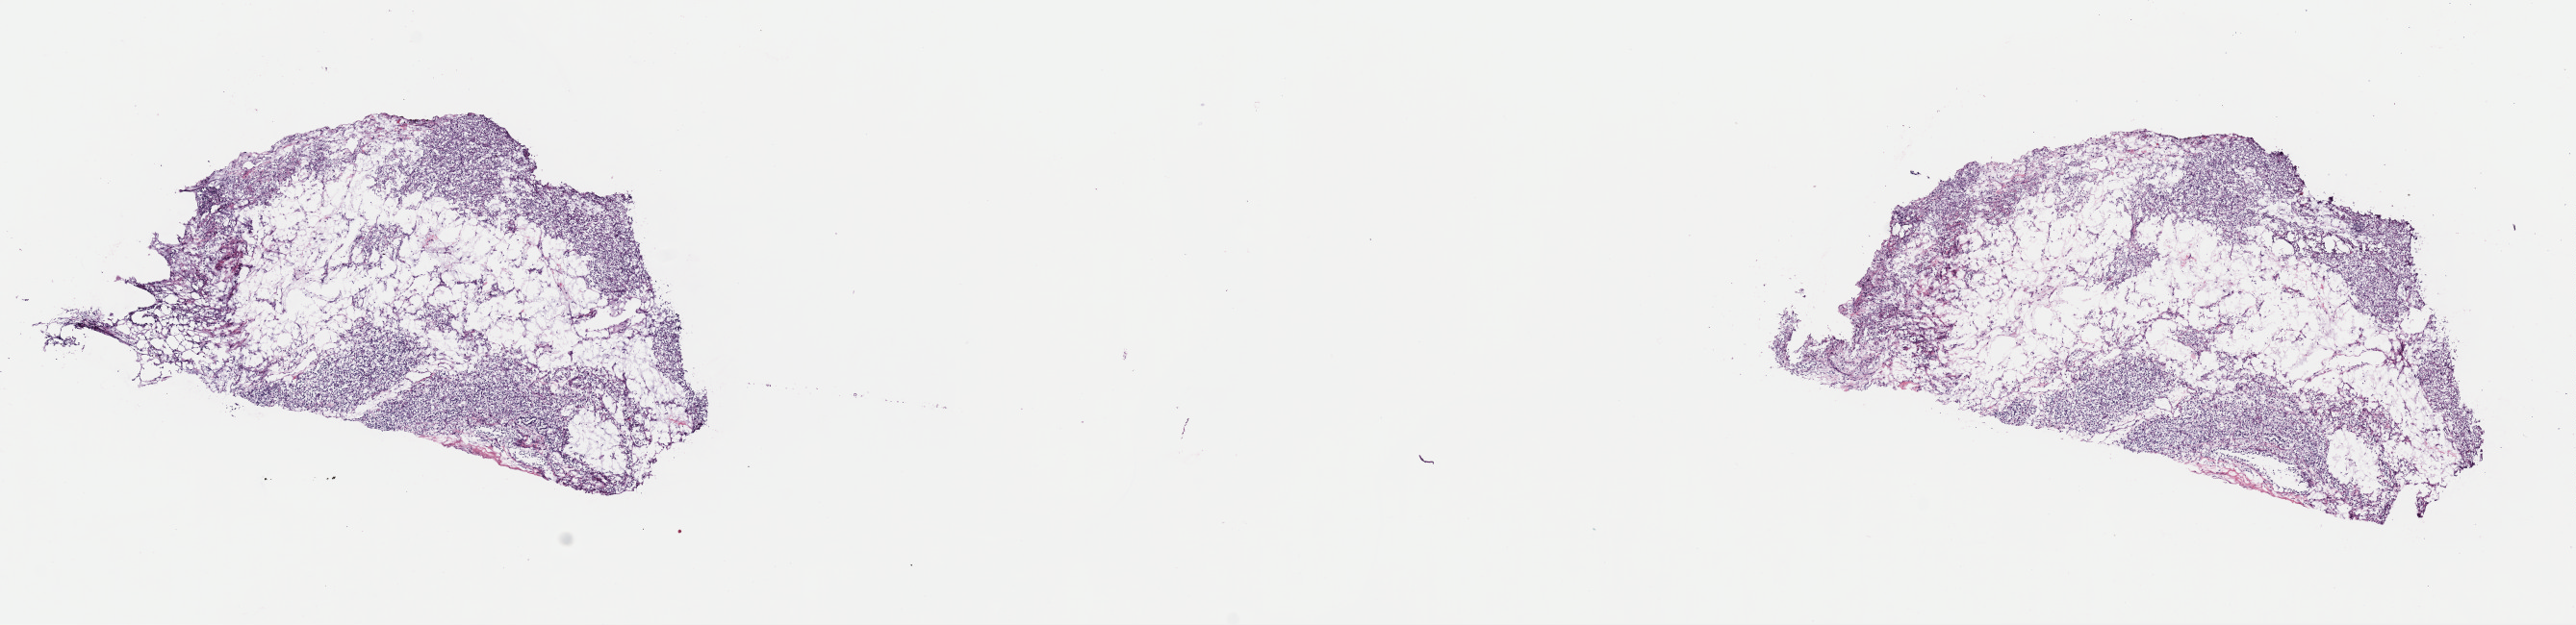
Hematoxylin and eosin (H&E) stained whole-slide image, a low-resolution overview of the entire scanned area, about 21.1 x 5.1 mm (slide scanned at 40x); frozen section from the top of the tissue portion; sample: primary tumour, kidney. Male, age 78 years at initial diagnosis. Histologic grade: G2 (moderately differentiated). Pathologist review of this section (percent, as recorded): tumour cells 85%, tumour nuclei 85%, normal cells 0%, stromal cells 15%, necrosis 0%. Inflammatory infiltration, as recorded: lymphocyte infiltration 0%, monocyte infiltration 0%, neutrophil infiltration 0%.
TNM: T1a NX MX. Diagnosis: Renal cell carcinoma, NOS. AJCC pathologic stage: I.